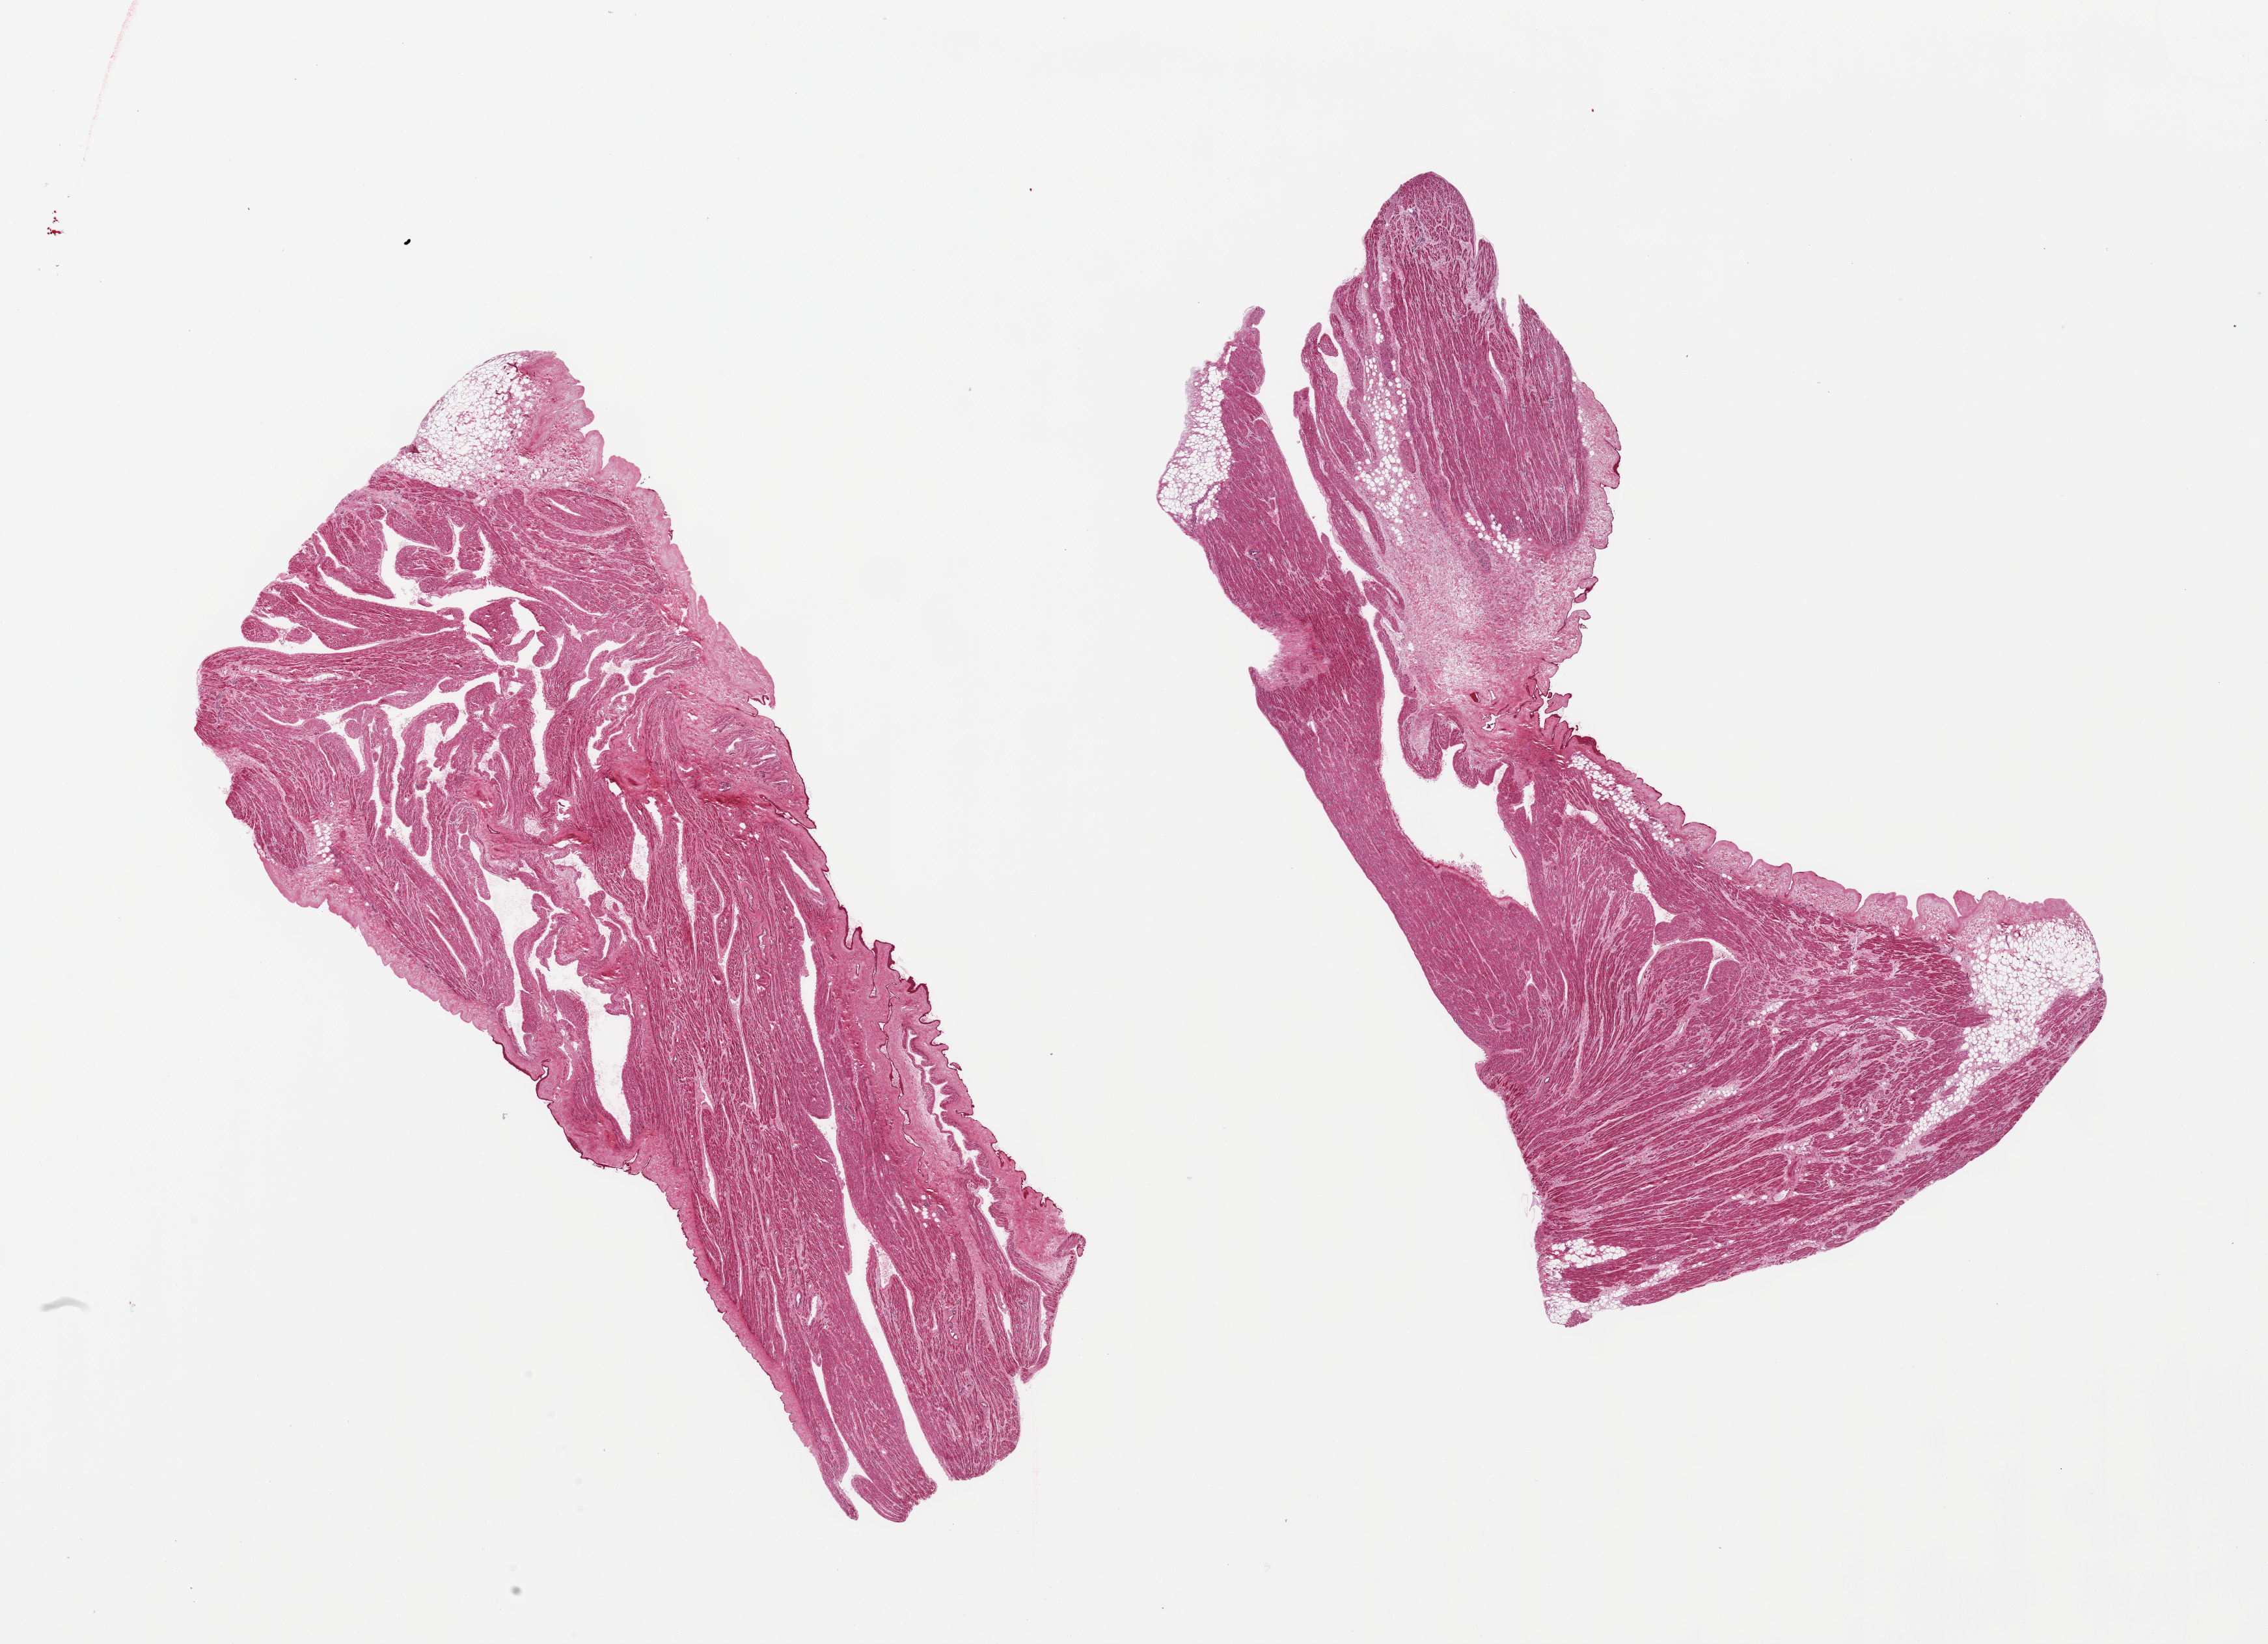
Digitized haematoxylin and eosin-stained section, brightfield — low-resolution overview of the scanned area, about 27.6 x 20.0 mm (acquisition: 20x scan); PAXgene-fixed paraffin-embedded (PFPE) section; sampled site (target tissue): auricular appendage; tissue donor sample. Donor sex: male.
Reviewer comment on this tissue sample: 2 pieces, no abnormalities.